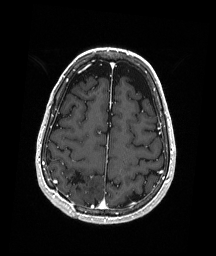
Brain MRI from a brain-tumour surgery series, one axial slice. Slice 63 of 192 in the series (ordered by position). T1-weighted post-contrast. 216 × 256 image matrix, field of view 211 × 250 mm. Case-level facts recorded for this patient, not image findings: histopathology: Astrocytoma; WHO grade: 3; IDH mutation: yes.
Outlined on this slice (outlined manually by an expert reader):
- previous resection cavity: box from (x=67, y=171) to (x=85, y=194) px